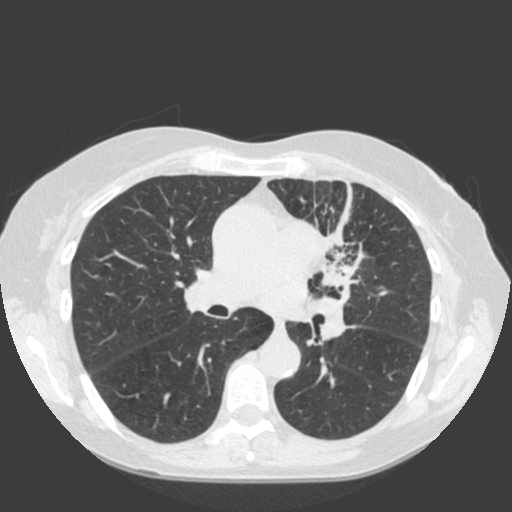
Low-dose screening chest CT, axial slice; baseline annual screen; lung window (W 1500 / L -600 HU); slice 75 of 184 in the series; 512 × 512 image matrix. Female, age 66 years at enrolment. Current smoker at enrolment.
Expert-annotated lung lesion, bounding box [x1, y1, x2, y2] px = [276, 200, 402, 314]. The exam's reader record, not a measurement of the box and not confirmed to be the same lesion: non-calcified nodule or mass ≥4 mm, left upper lobe, 61 × 45 mm, spiculated (stellate) margins, soft tissue attenuation.